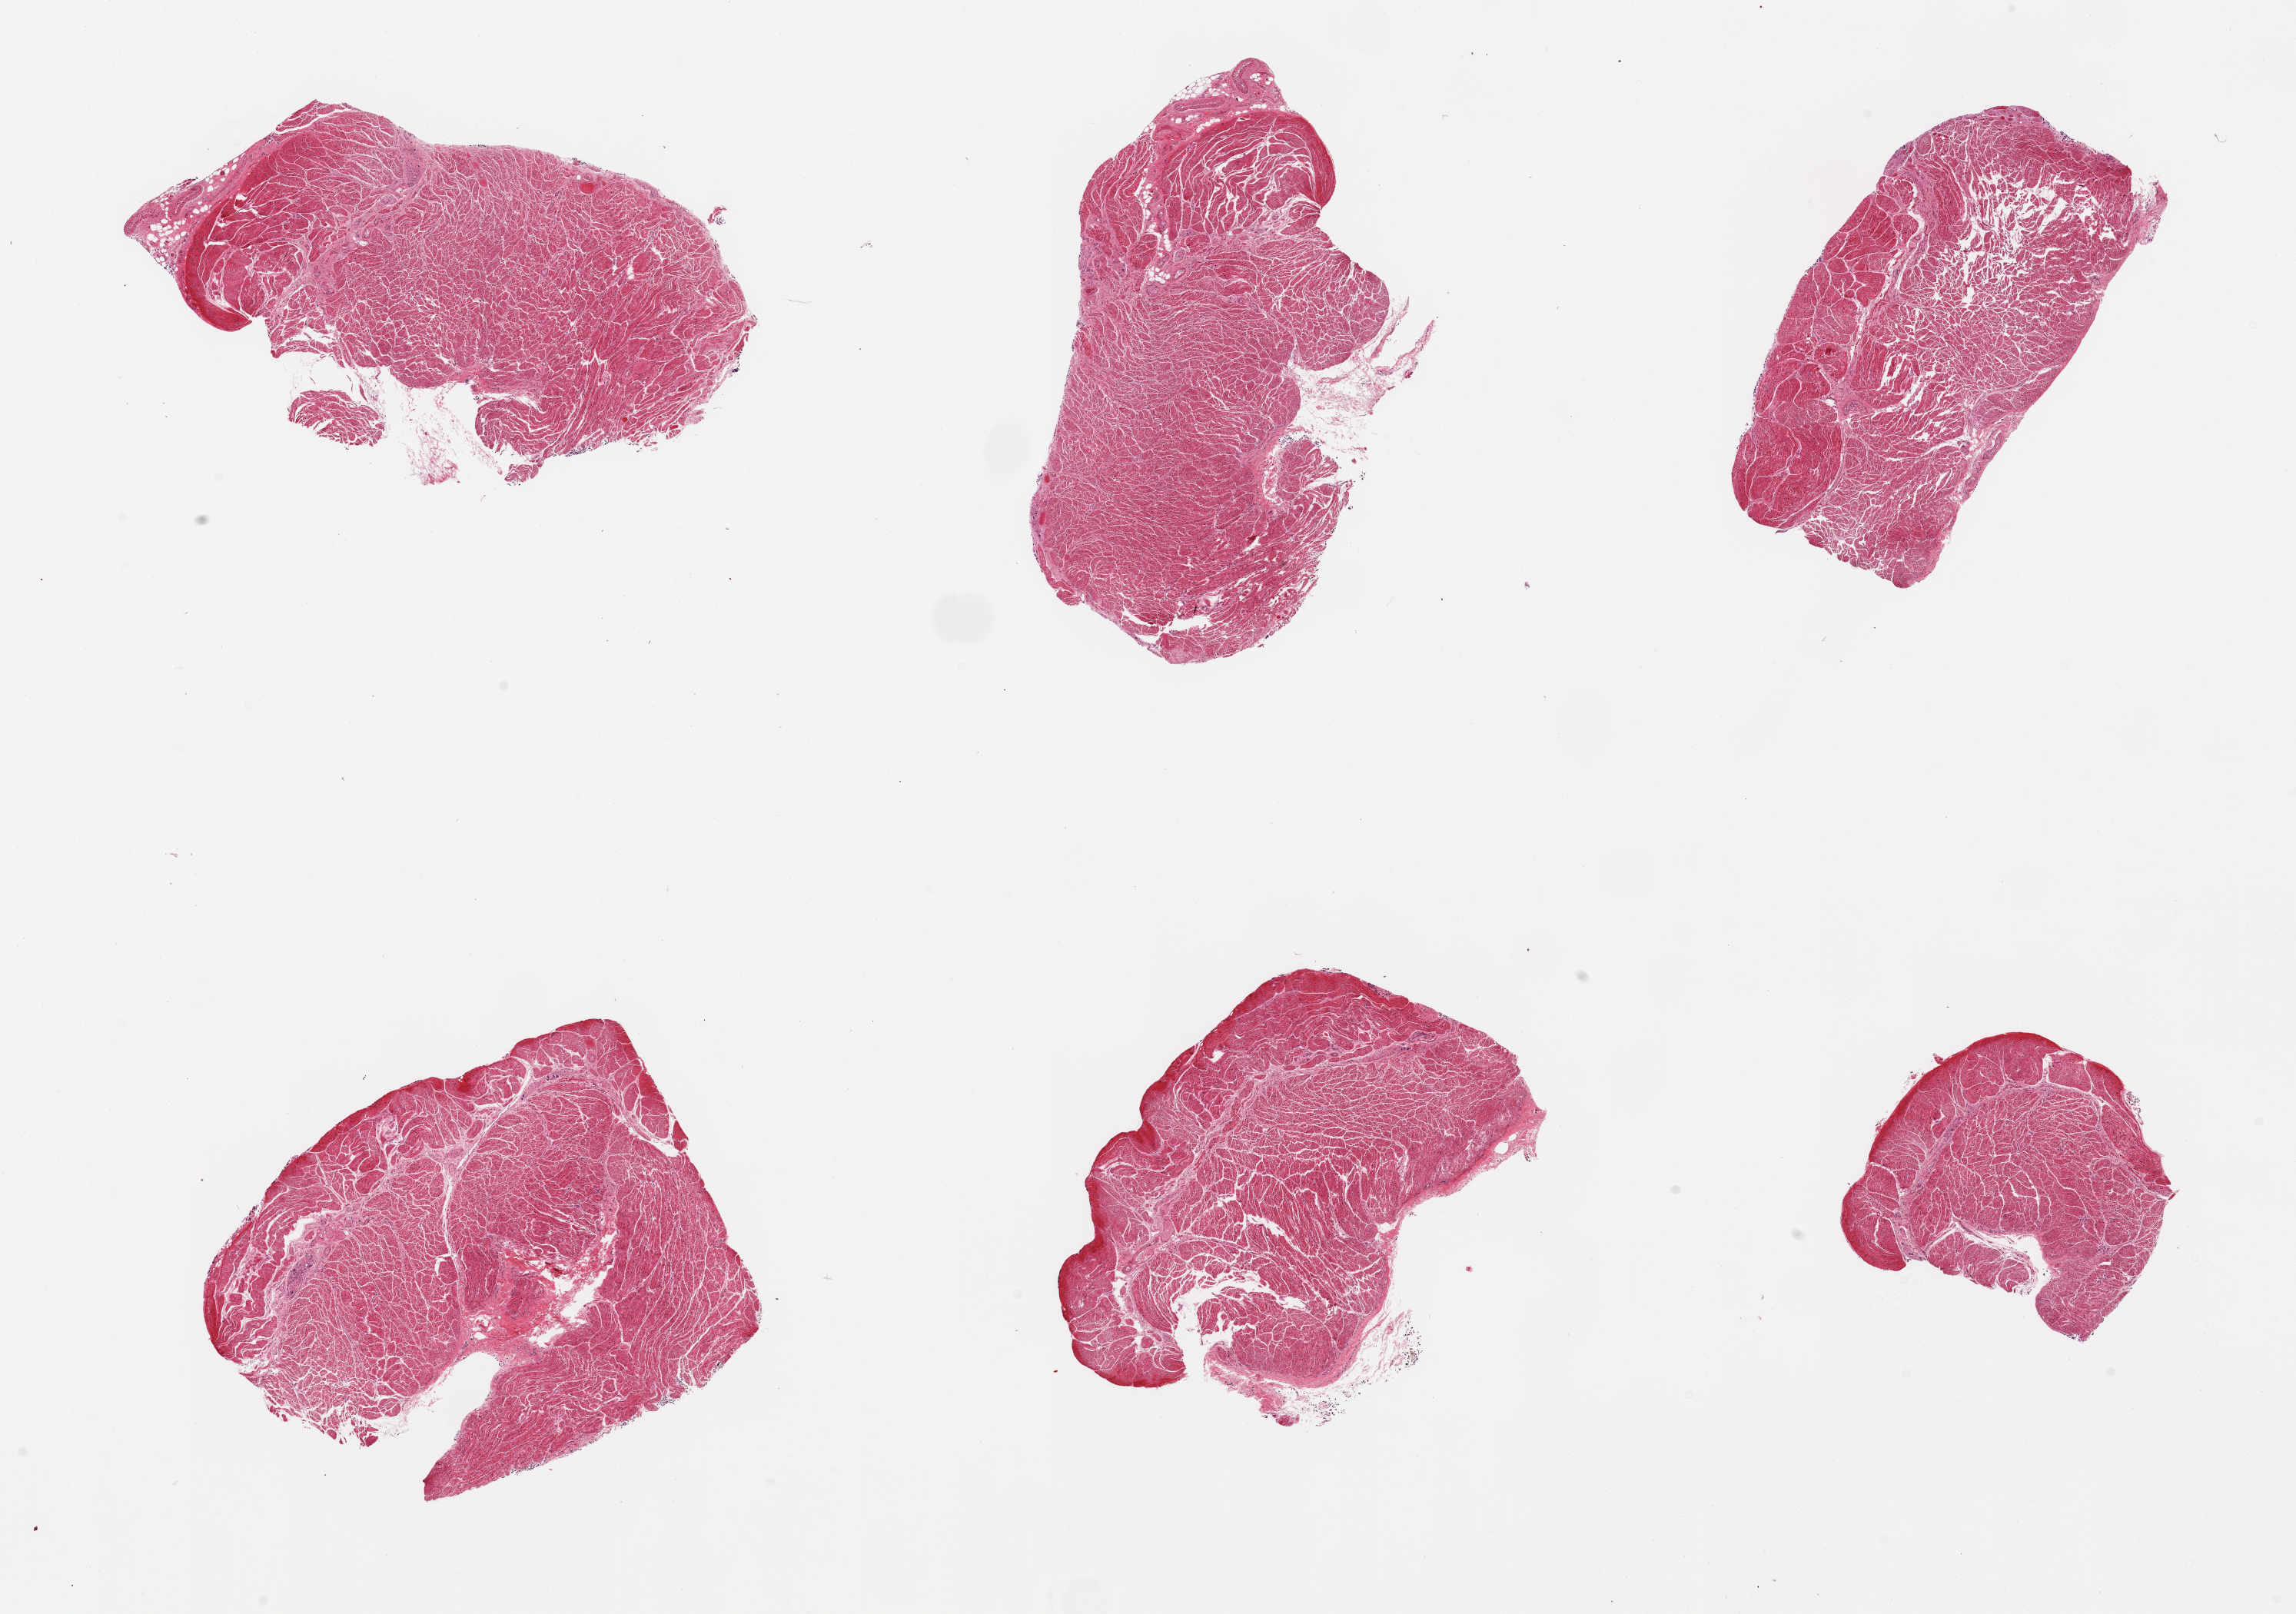
Whole-slide image, hematoxylin and eosin (H&E) stain, brightfield, low-resolution overview of the scanned area, about 23.6 x 16.6 mm (acquisition: 20x scan); PAXgene-fixed, paraffin-embedded tissue; sampled site (target tissue): esophageal muscle; donor tissue sample. Donor: male.
* pathologist's review note for this sample: 6 pieces; well trimmed